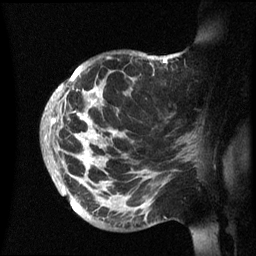
Breast MRI (dynamic contrast-enhanced), one sagittal slice; position 42 of 60 along the scan axis; dynamic contrast-enhanced series, image 2 of 3 at this slice position (ordered by acquisition); 1.5 T; TE 4.2 ms, TR 8.4 ms; 2.4 mm slice thickness; 256 × 256 image matrix, field of view 230 × 230 mm. Female patient, age 48 years.
Structures marked on this image (semi-automatic segmentation, software-assisted and operator-edited):
- analysis volume of interest (the breast-tissue region the enhancement analysis was run in; not a lesion): box from (x=43, y=52) to (x=202, y=236) px
- tumour enhancement mask (voxels above the 70 % enhancement threshold inside the analysis volume of interest): (x=45, y=56)–(x=173, y=194)